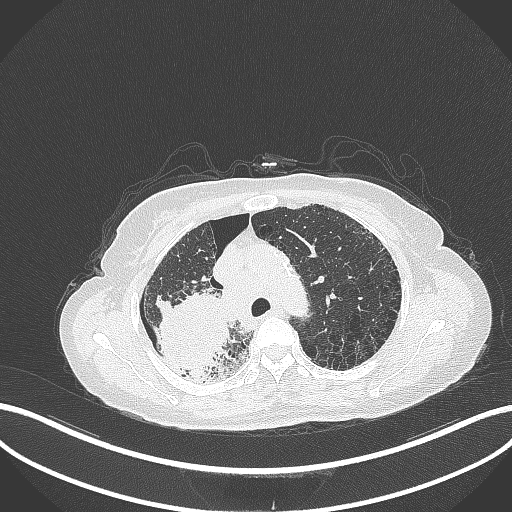
Chest CT, one axial slice; position 257 of 408 along the scan axis; reconstruction kernel B70f; lung window (W 1500 / L -600 HU); 1 mm slice thickness; 512 × 512 image matrix. Patient: female, 64 years. Case-level facts recorded for this patient, not image findings: clinical TNM (as recorded): T3 N3 M0.
Structures marked on this image (rectangle marked by the reading radiologist):
- lung tumour (recorded histology: squamous cell carcinoma): bounding box [x1, y1, x2, y2] px = [151, 286, 236, 379]